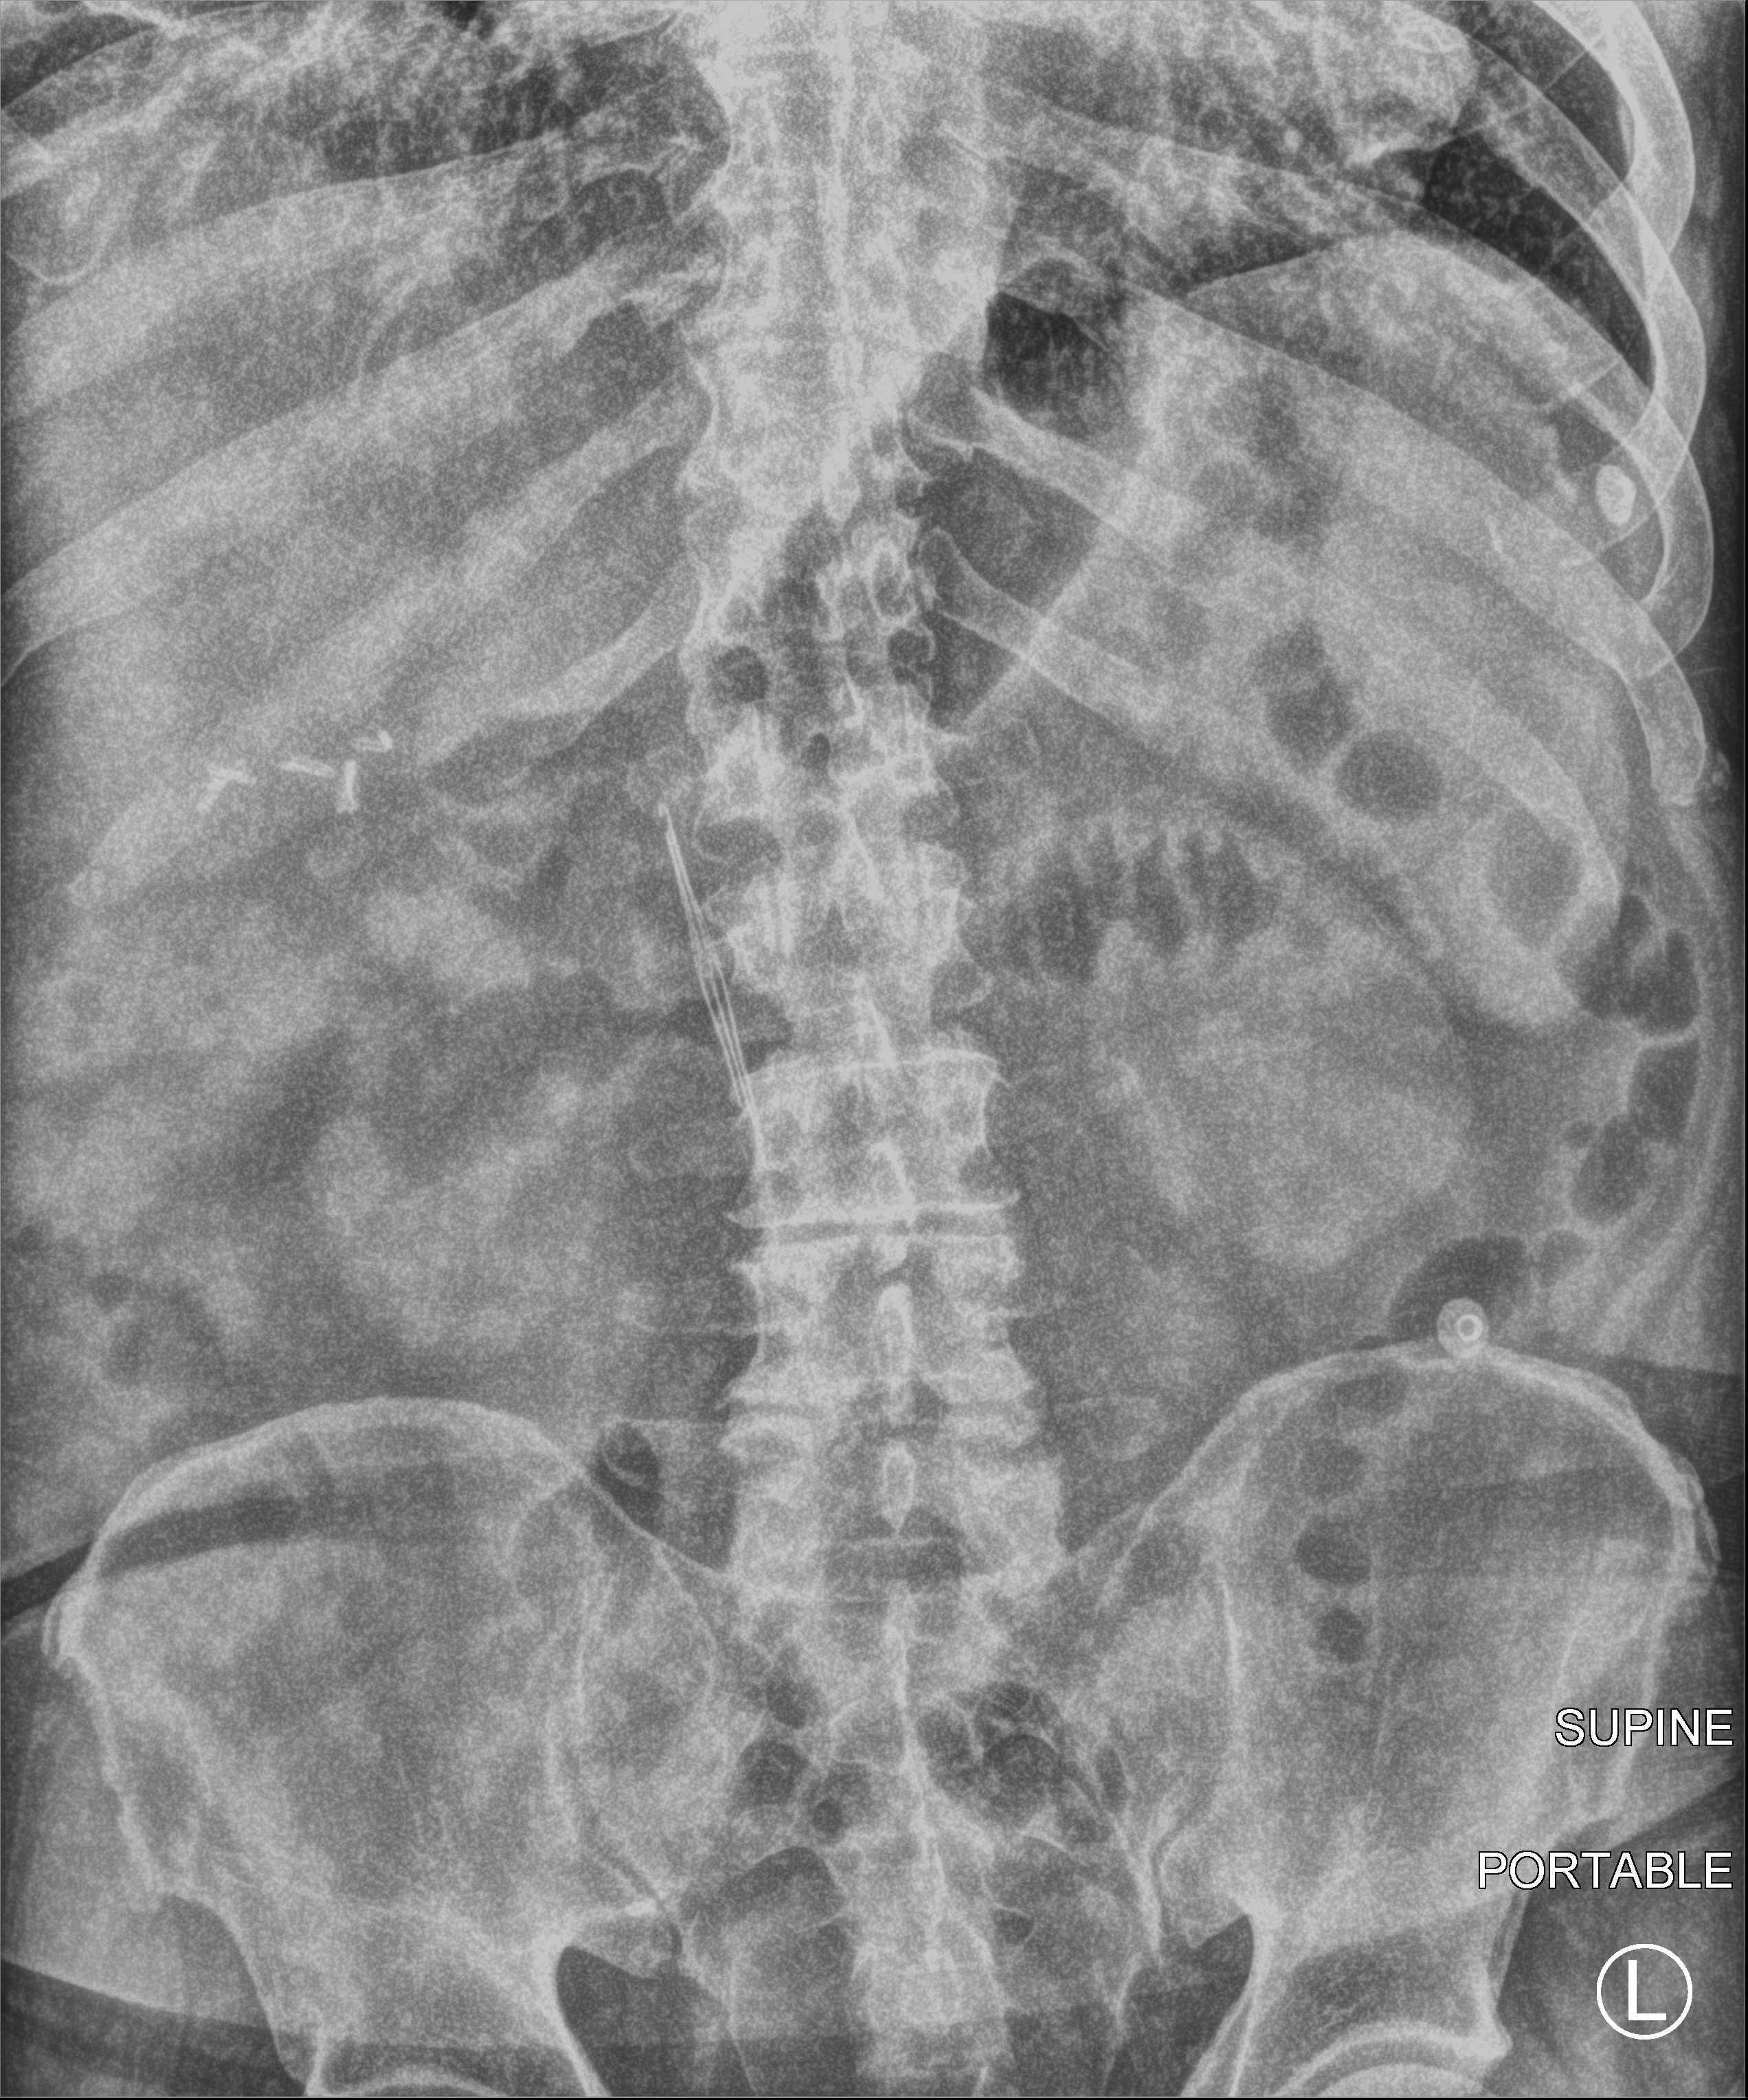
Bedside abdomen radiograph (computed radiography). Patient hospitalised with COVID-19; male, aged 60–74 years.
From the hospital-stay record, not from the radiograph (when in the stay this image was taken is not recorded): mechanically ventilated during this hospital stay: no.